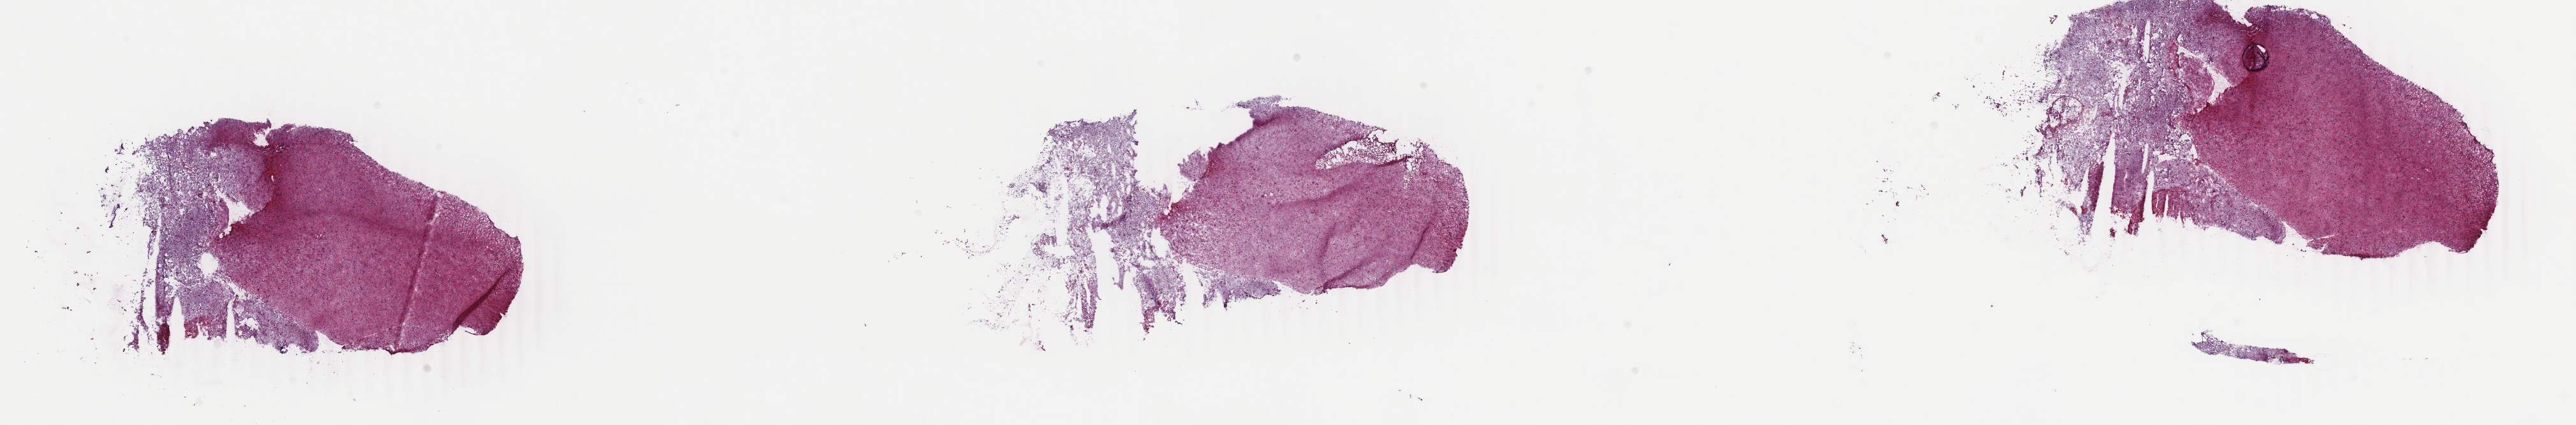
Digitized H&E-stained tissue section (whole slide) — low-resolution overview of the scanned area, about 32.1 x 5.3 mm (from a 40x scan). Frozen section. Primary tumour sample from the brain. Female, age 37 years at initial diagnosis. Composition of this section per pathologist review: tumour cells 50%, tumour nuclei 80%.
Pathologic diagnosis: Astrocytoma, anaplastic (cerebrum).